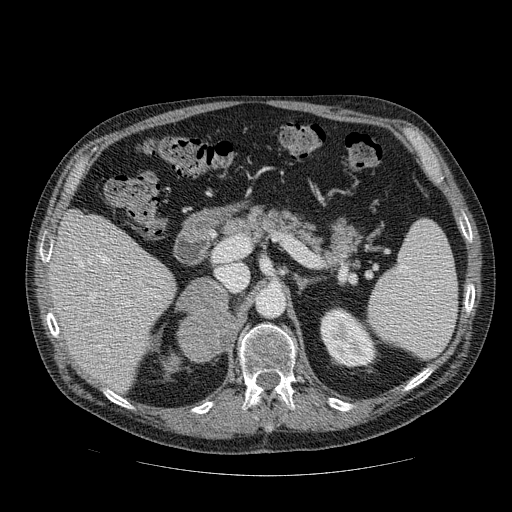
Contrast-enhanced abdominal CT, one axial slice. 120 kVp. Intravenous contrast given. Soft-tissue window (W 400 / L 40 HU). 512 × 512 image matrix. Patient: male, 56 years. From the clinical record (not read from this slice): diagnosis: adrenocortical carcinoma; tumour side: right adrenal; tumour size at pathology: 9 cm; Ki-67 index: 48 %; stage (as recorded): 4.
Annotated regions visible in this slice (semi-automatic segmentation, software-assisted and operator-edited):
- mass: bounding box <180,280,234,360> (left, top, right, bottom; pixels)